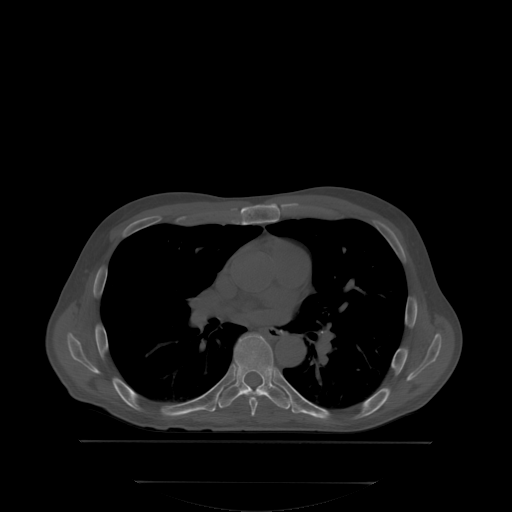
CT including the spine, one axial slice. Slice 230 of 350 in the series (ordered by position). Bone window (W 1800 / L 400 HU). 512 × 512 image matrix, field of view 500 × 500 mm. Patient: male, 58 years. From the clinical record (not read from this slice): primary cancer: prostate.
Annotated regions visible in this slice (semi-automatically segmented with operator editing):
- T6 vertebra: bounding box [x1, y1, x2, y2] px = [247, 384, 289, 416]
- T7 vertebra: [218, 333, 291, 408]